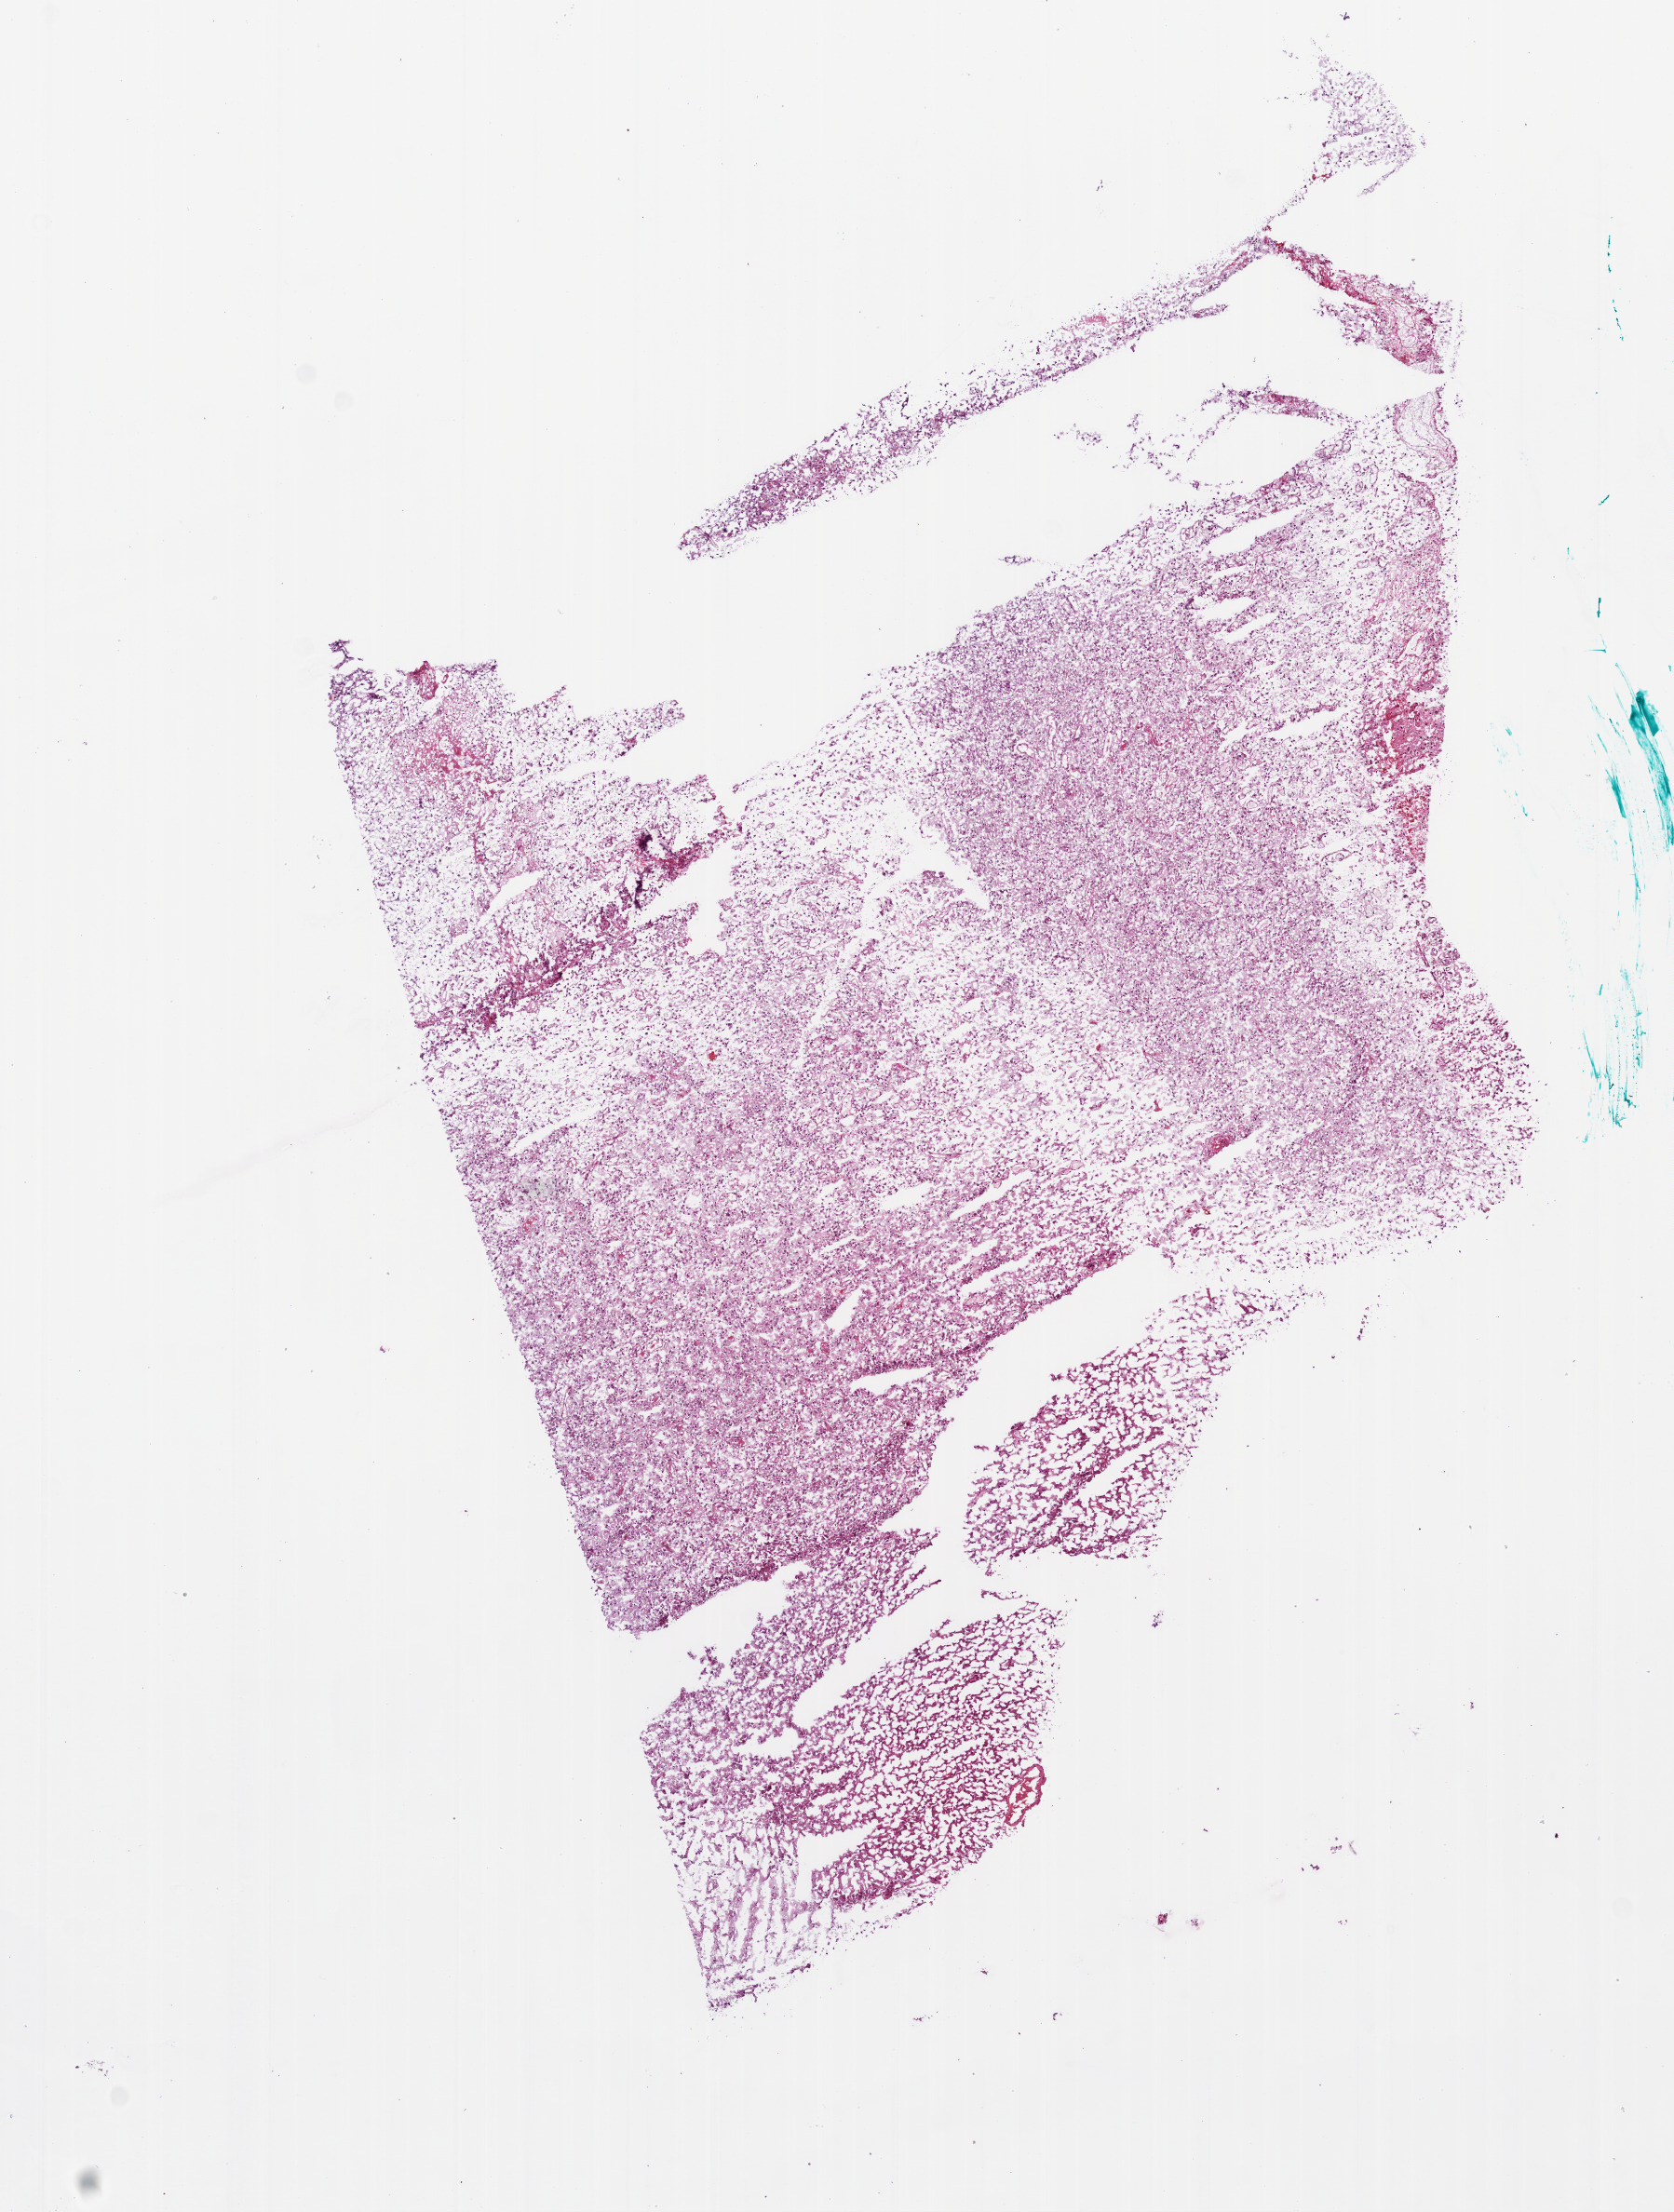
H&E whole-slide image, whole scanned area (about 7.3 x 9.6 mm, from a 20x scan) shown as a low-resolution overview, frozen section from the bottom of the tissue portion, sample: primary tumour, brain. Male patient; age at initial diagnosis 46 years. Composition of this section per pathologist review: tumour cells 90%, tumour nuclei 95%, normal cells 0%, stromal cells 0%, necrosis 10%. Inflammatory infiltration, as recorded: neutrophil infiltration 100%.
* histologic diagnosis: Glioblastoma